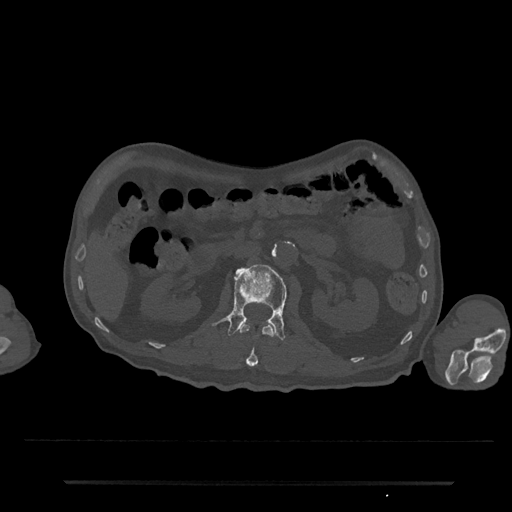
CT including the spine, one axial slice; position 85 of 797 along the scan axis; 120 kVp; bone window (W 1800 / L 400 HU); 0.5 mm slice thickness; 512 × 512 image matrix, field of view 427 × 427 mm. Patient: male, 74 years. Case-level facts recorded for this patient, not image findings: primary cancer: prostate.
Structures marked on this image (semi-automatically segmented with operator editing):
- L1 vertebra: bounding box (x1, y1, x2, y2) in pixels: (239, 321, 274, 367)
- L2 vertebra: (212, 264, 287, 341)